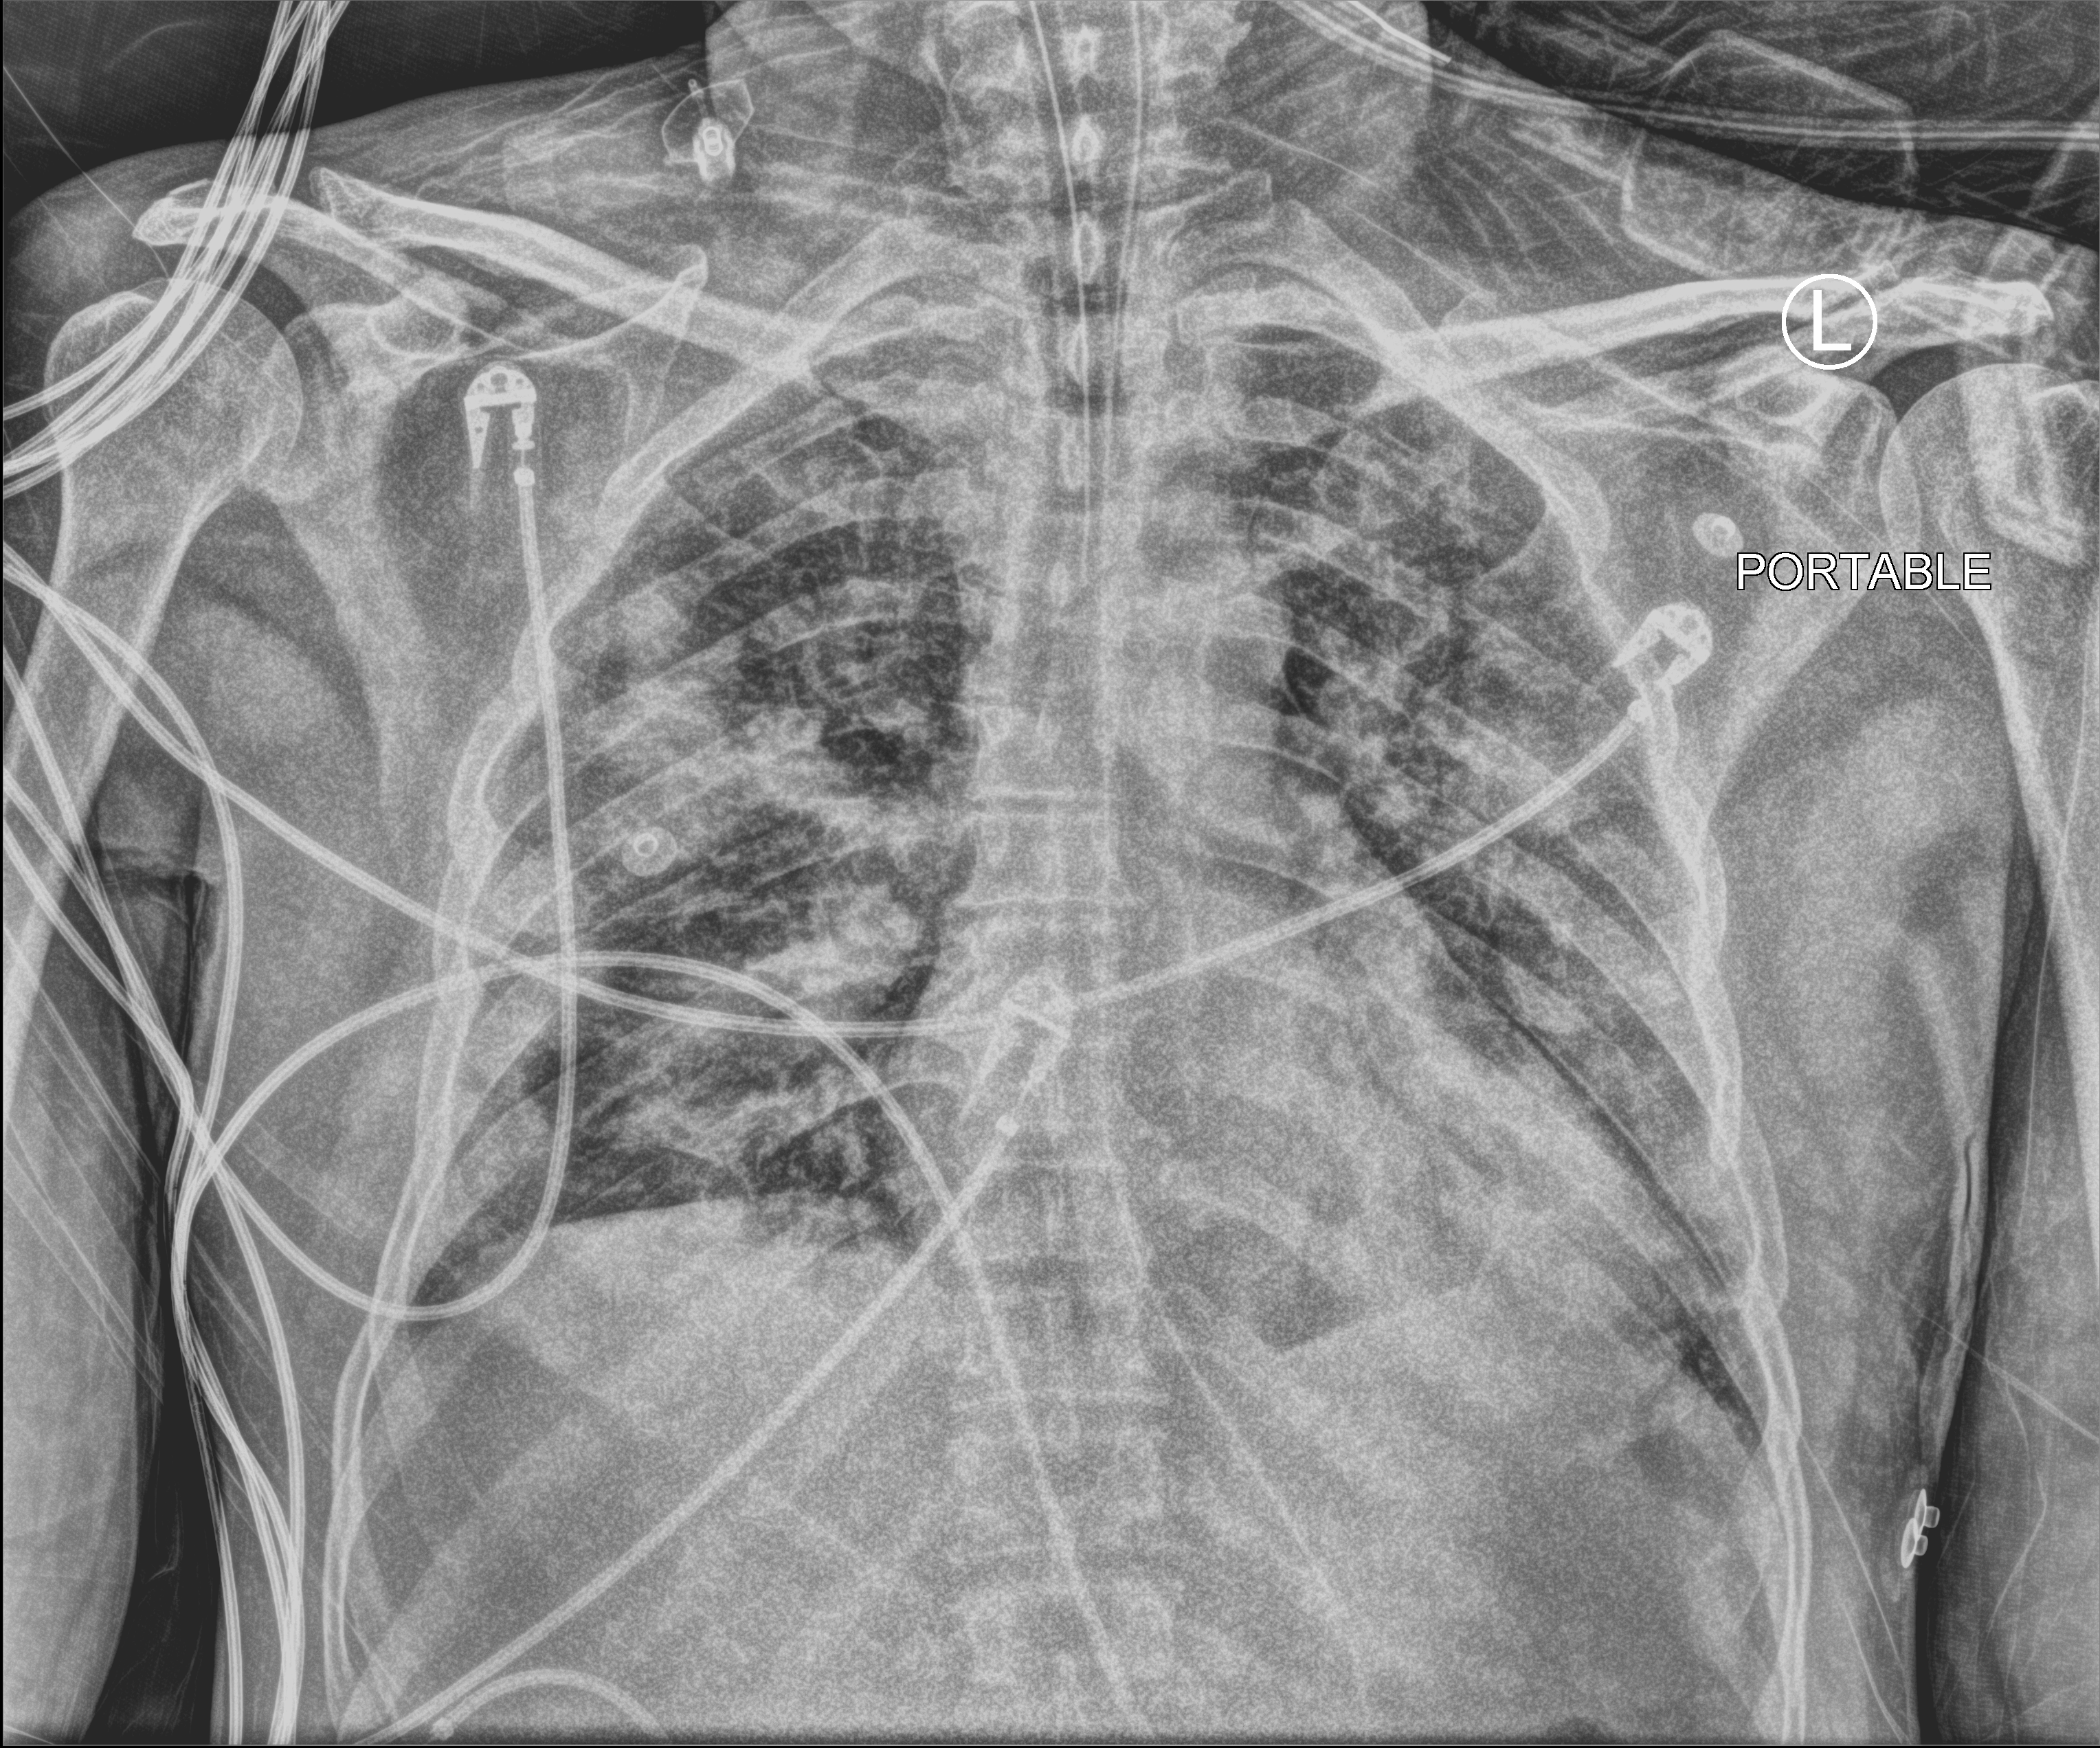
Bedside chest radiograph (computed radiography); anteroposterior (AP) projection. Male patient hospitalised with COVID-19, age 18–59 years.
Hospital-stay facts (about this admission, not read from this image; timing relative to this image not recorded):
- diabetes (admission record): no
- mechanically ventilated during this hospital stay: yes
- smoking status (admission record): never